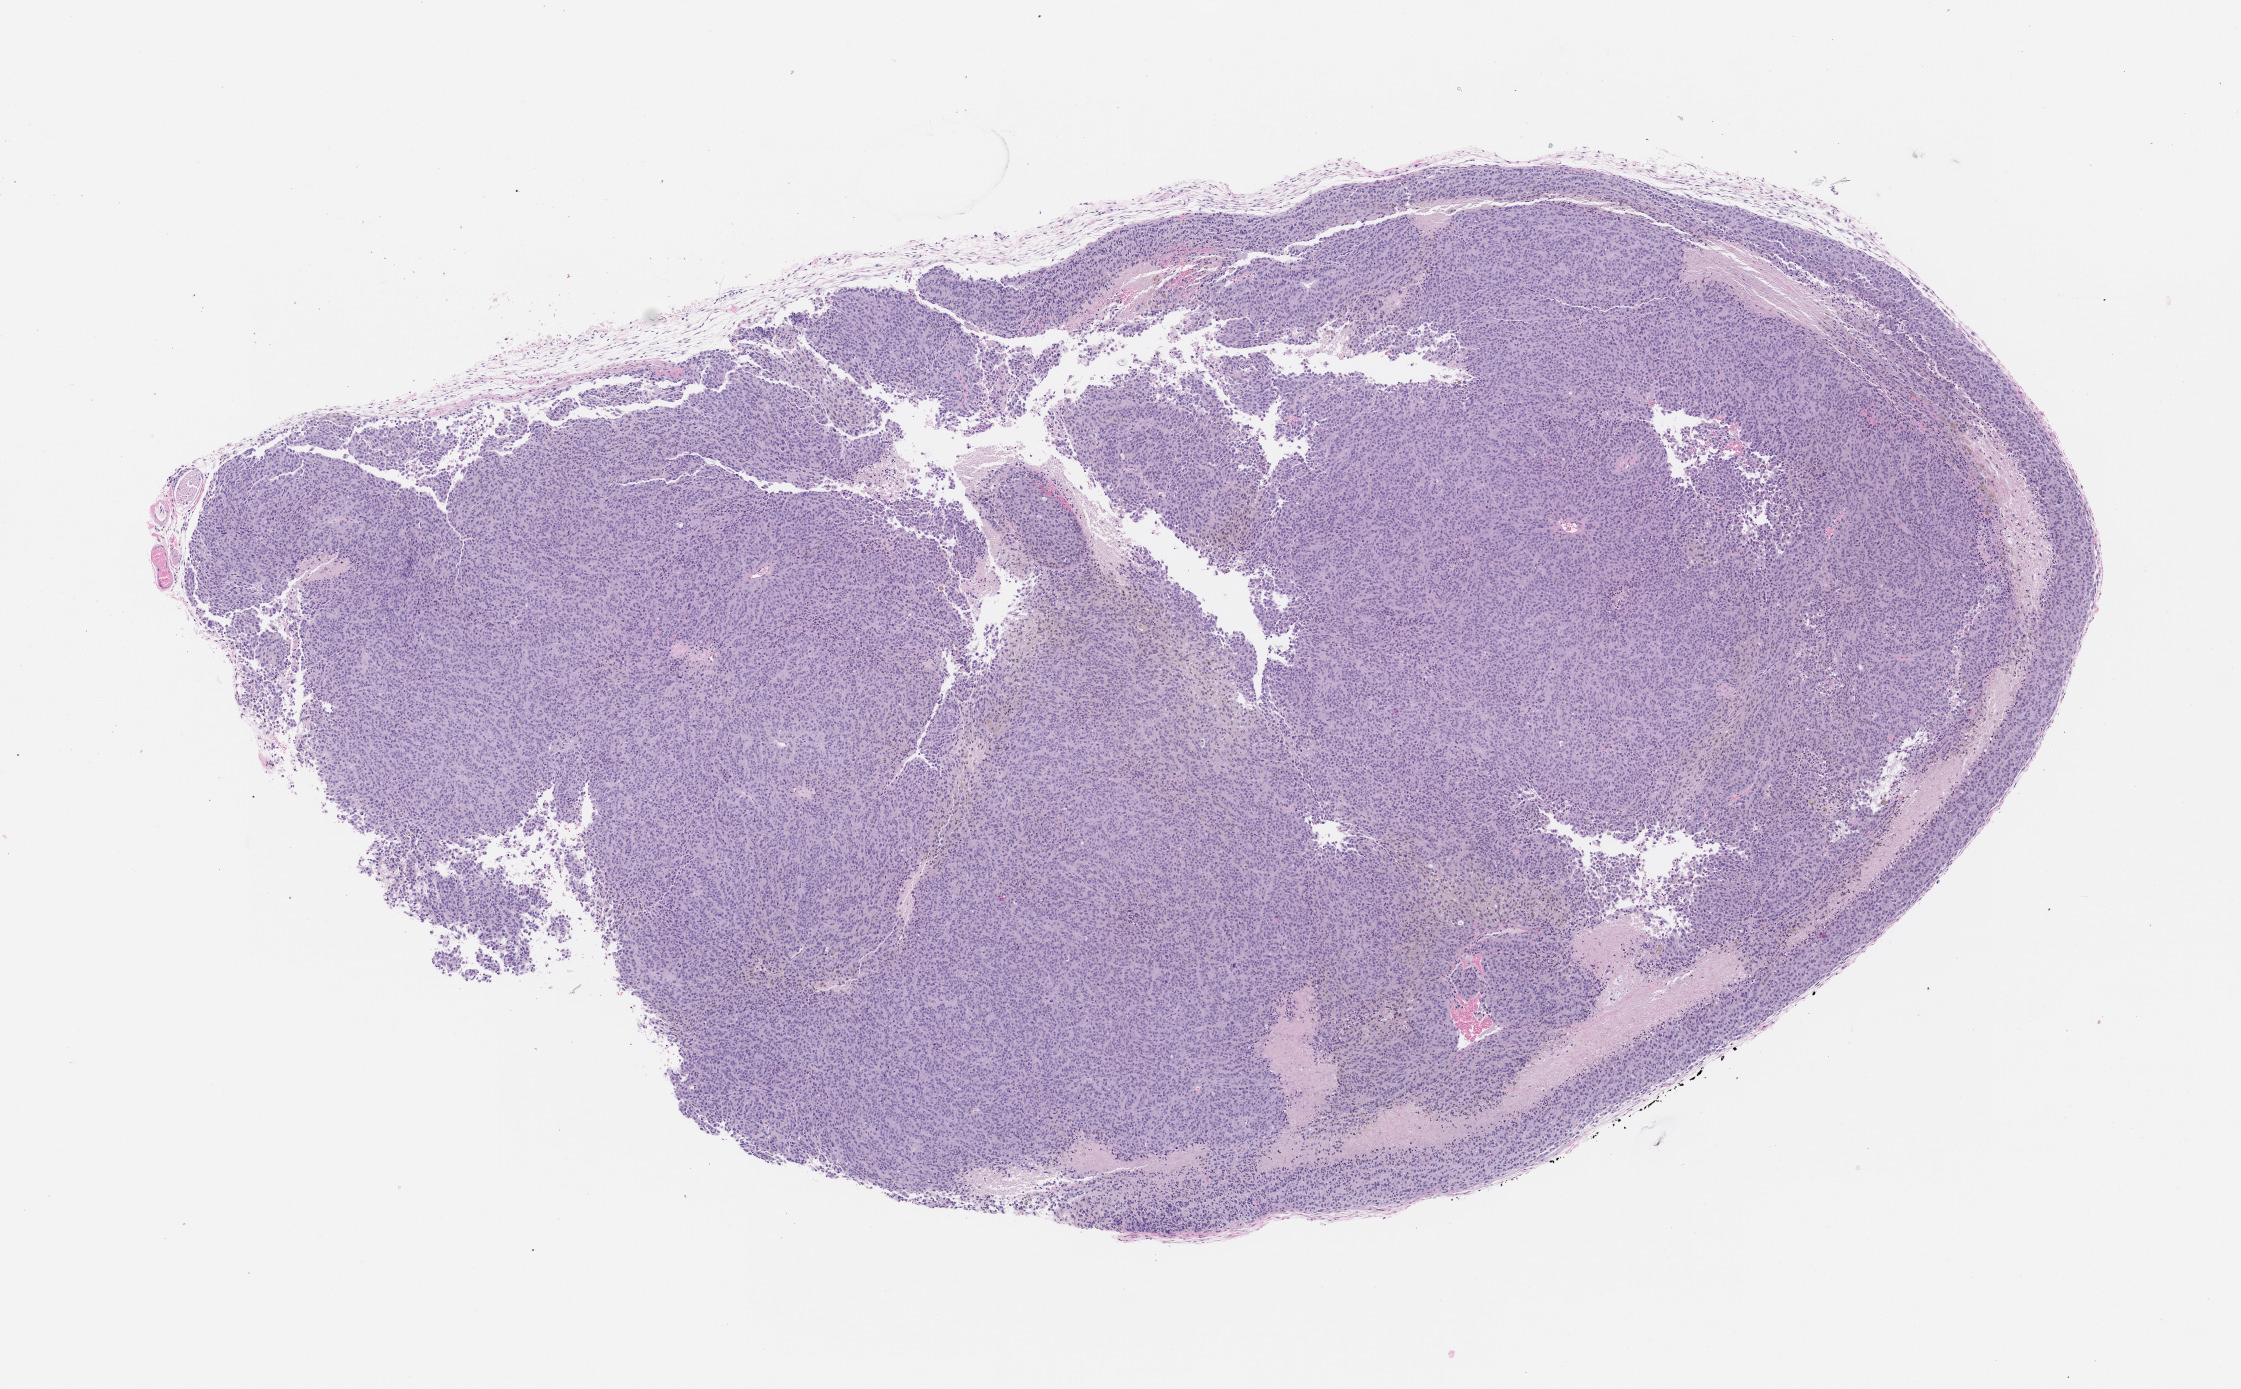
Whole-slide image, H&E: patient-derived xenograft (human tumor grown in a mouse), passage 1 — shown as a low-resolution overview of the whole scanned area (about 9.0 x 5.6 mm); FFPE section; originating tumor site category: skin.
Originating patient diagnosis: Melanoma.